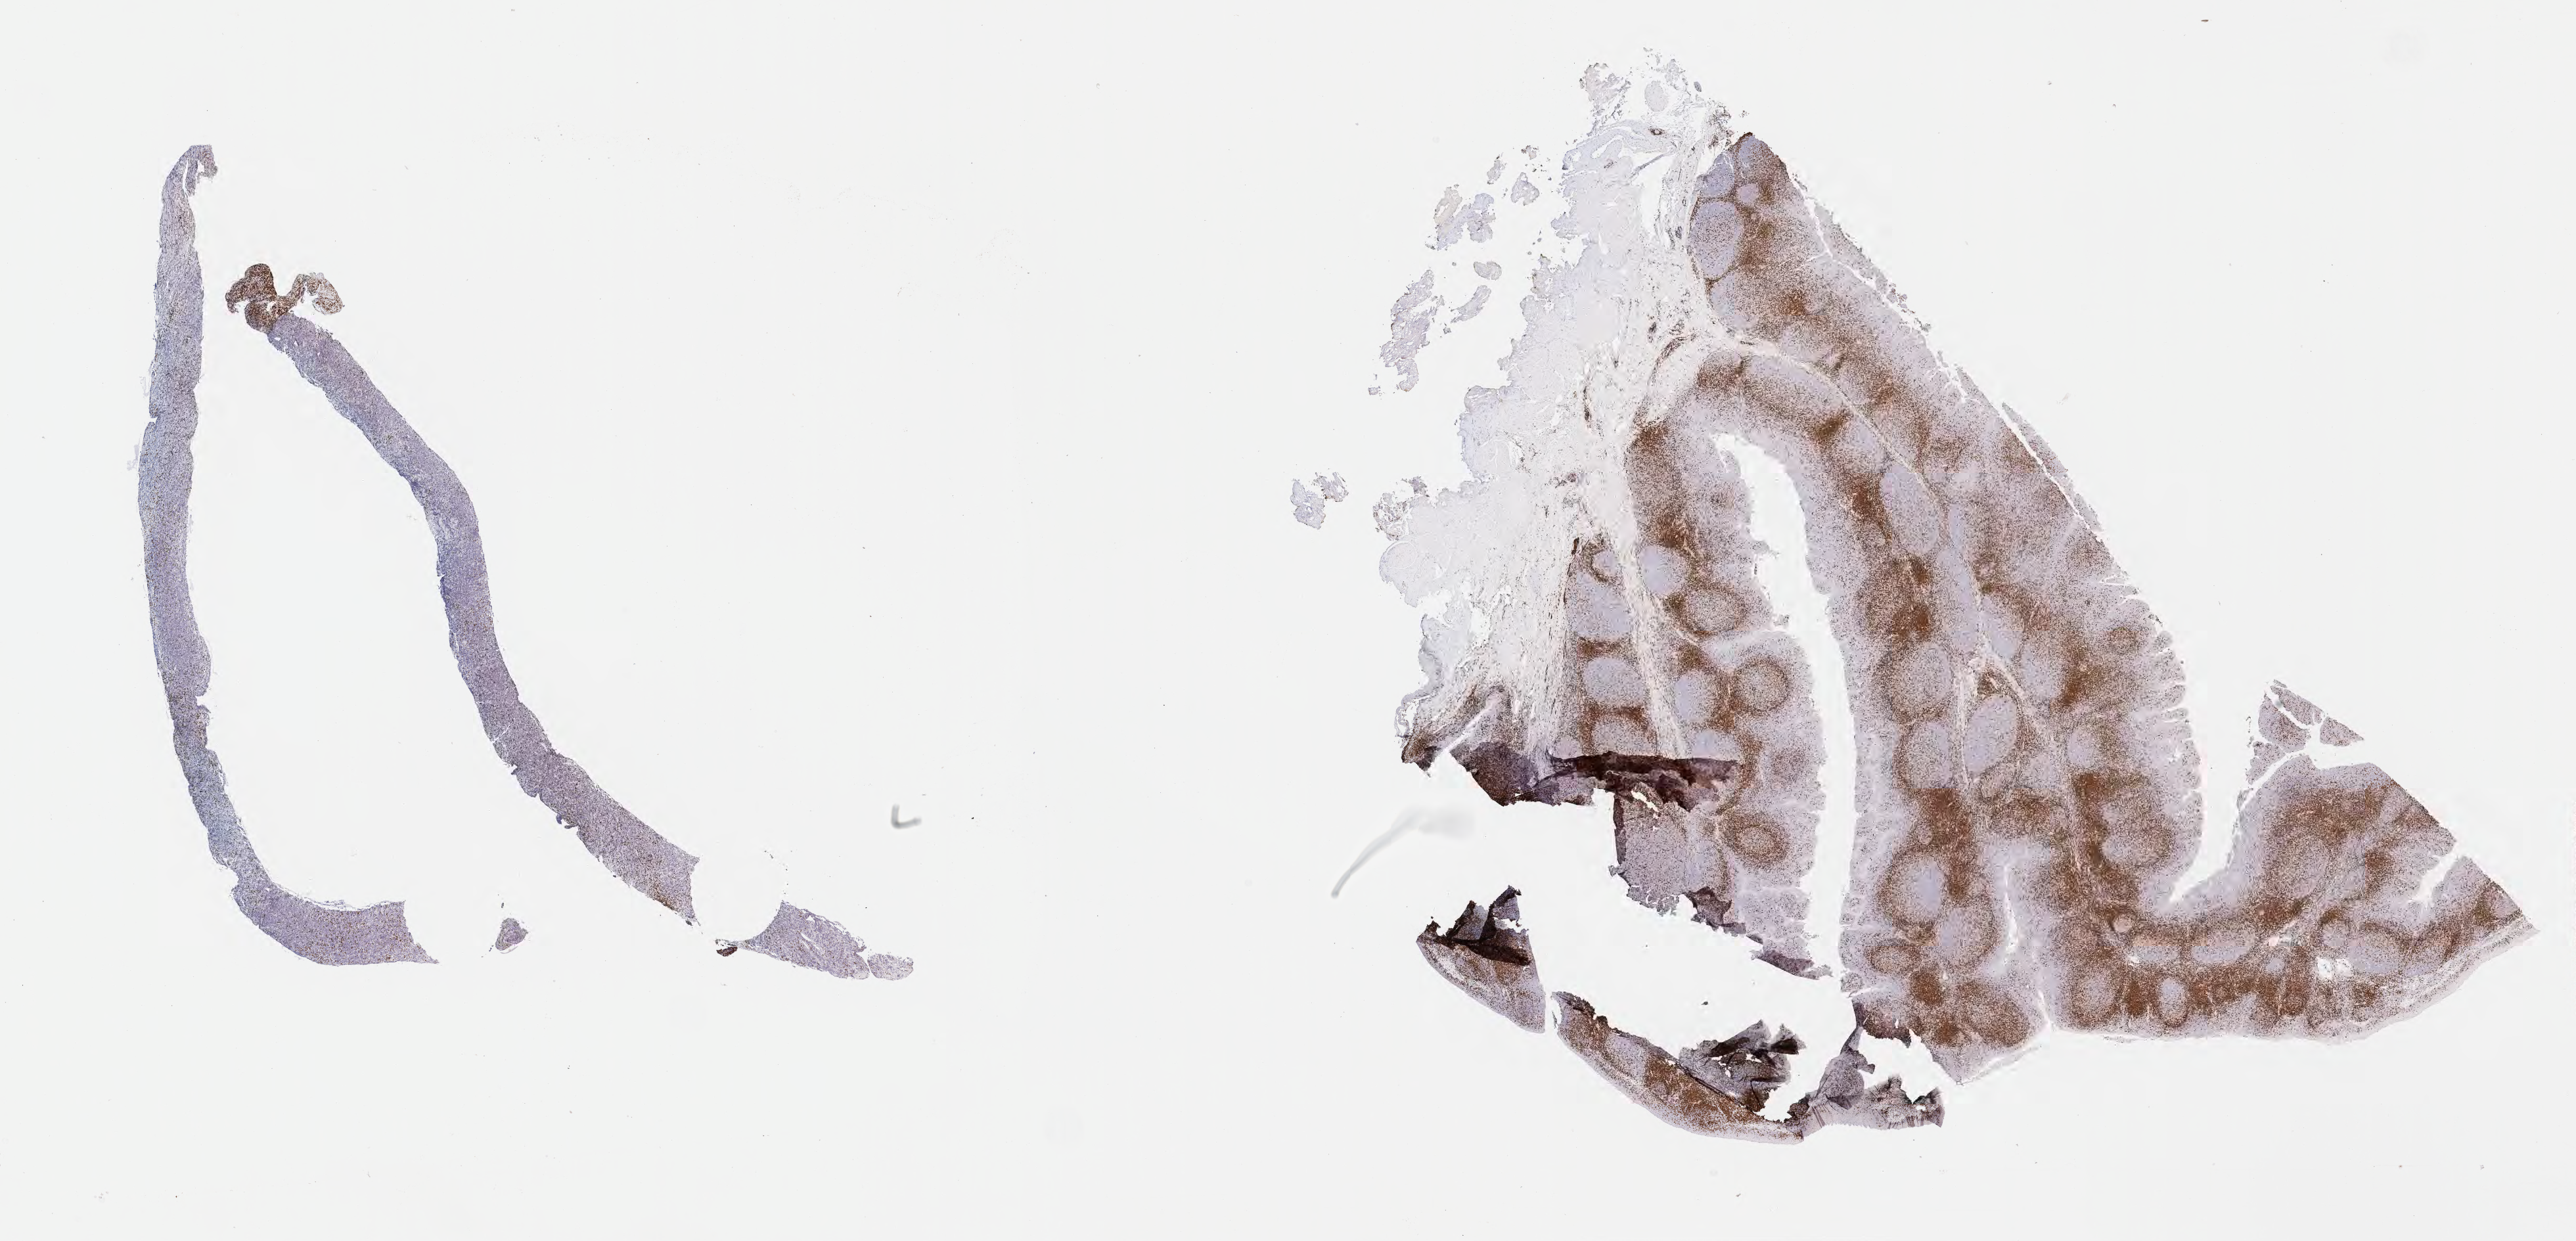
IHC for CD3, whole-slide image — shown as a low-resolution overview of the whole scanned area (about 31.7 x 15.3 mm); specimen: tumor tissue; anatomic site: abdomen proper. Patient: male, age at initial diagnosis 9 years.
Diagnosis: Burkitt lymphoma, NOS.